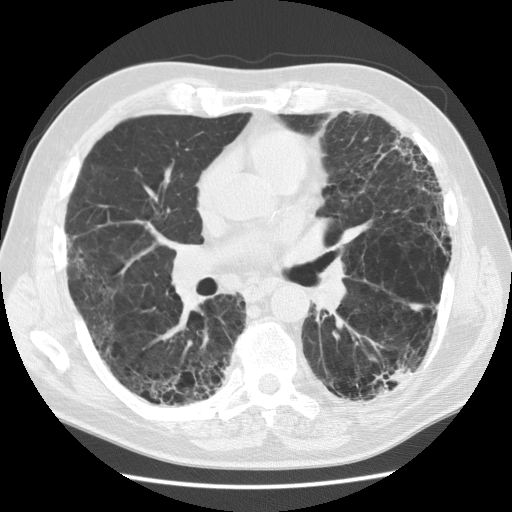
Low-dose screening chest CT, one axial slice. Slice 66 of 128 in the series (ordered by position). Reconstruction kernel STANDARD. 120 kVp. Lung window (W 1500 / L -600 HU). 2.5 mm slice thickness. 512 × 512 image matrix, field of view 360 × 360 mm.
Structures marked on this image (outlined manually by an expert reader):
- lesion 1 (tumor, lower lobe of left lung): bounding box [x1, y1, x2, y2] px = [387, 367, 412, 386]